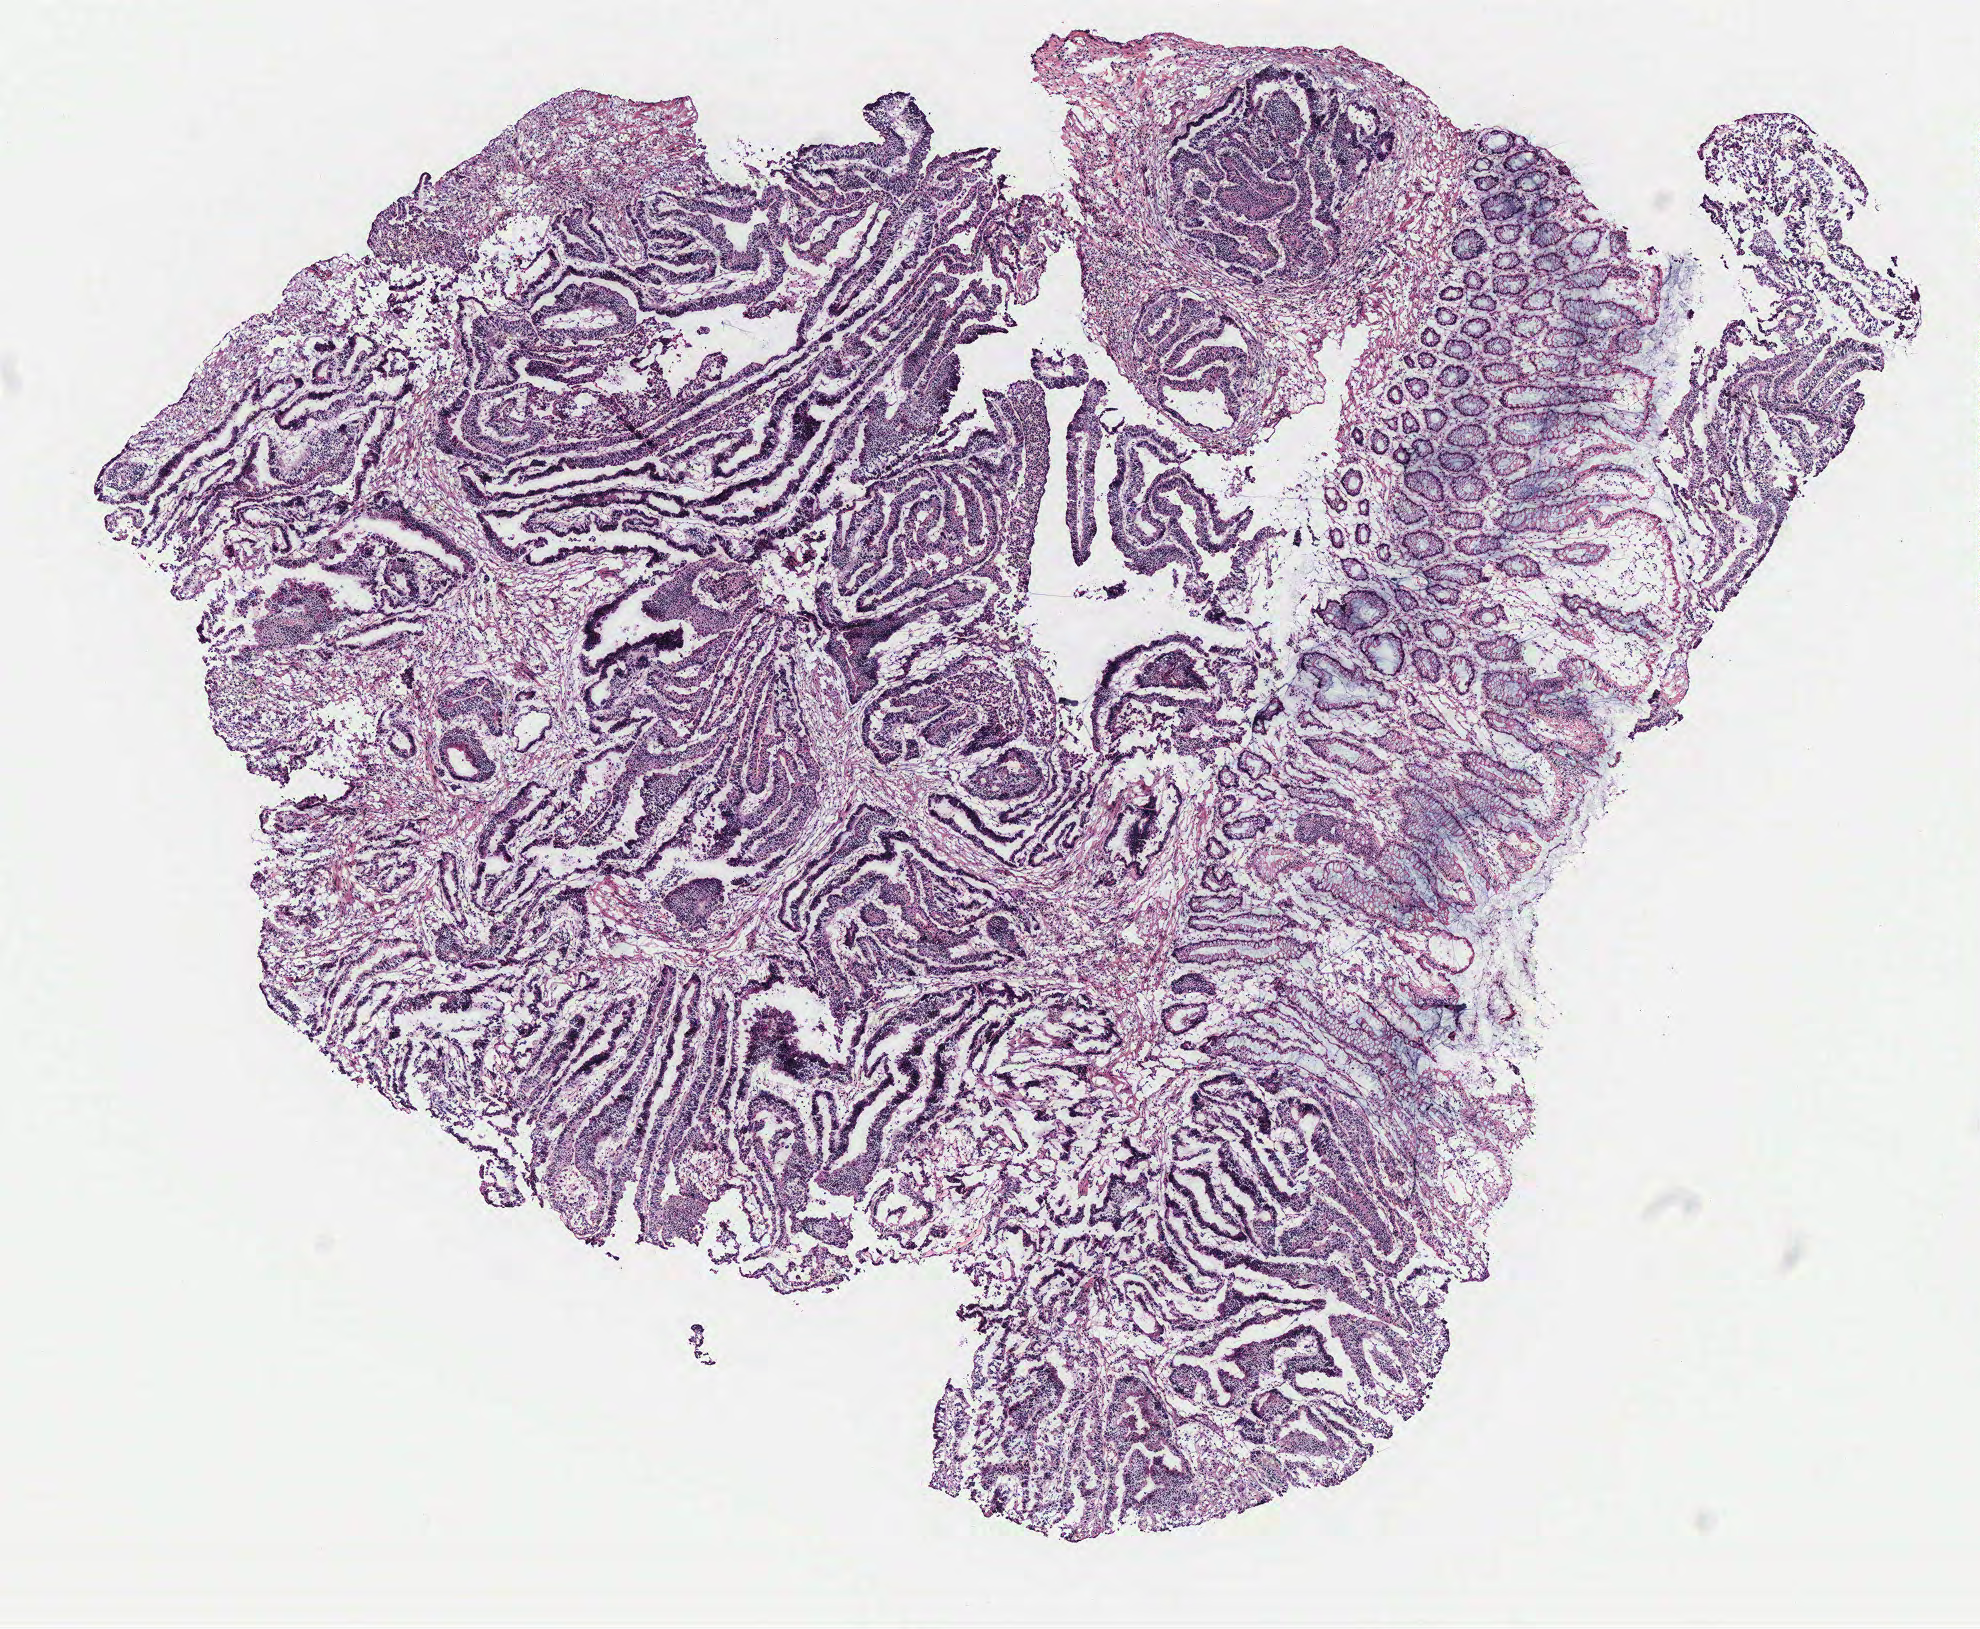
Digitized H&E-stained tissue section (whole slide), shown as a low-resolution overview of the whole scanned area (about 7.9 x 6.5 mm, slide scanned at 40x). Colon, tissue type not recorded.
Patient diagnosis (cohort enrolment): colon cancer (colon).